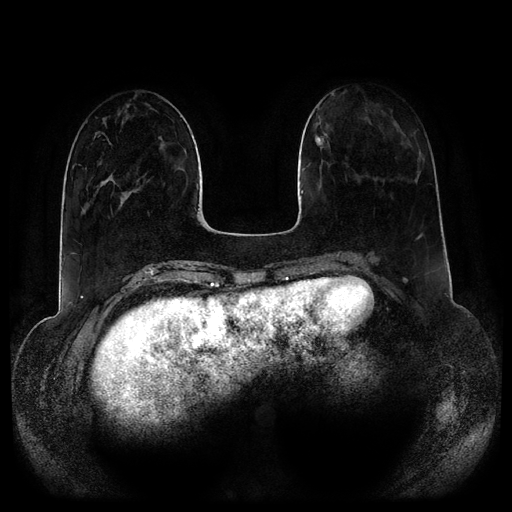
Breast MRI (dynamic contrast-enhanced, multi-phase), one axial slice. Slice 35 of 116 in the series (ordered by position). Dynamic contrast-enhanced series, time point 2 of 5 at this slice position (early post-contrast). 1.5 T. TE 2.5 ms, TR 5.2 ms. 2 mm slice thickness. 512 × 512 image matrix, field of view 390 × 390 mm. Patient: female, 34 years.
Outlined on this slice (semi-automatically segmented with operator editing):
- breast lesion (labelled benign in the annotation): bounding box [x1, y1, x2, y2] px = [315, 128, 329, 149]